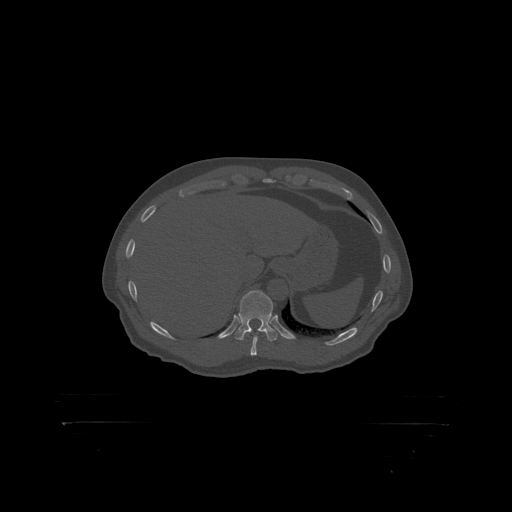
CT including the spine, one axial slice. Position 386 of 399 along the scan axis. 120 kVp. Bone window (W 1800 / L 400 HU). 1.25 mm slice thickness. 512 × 512 image matrix, field of view 650 × 650 mm. Patient: male, 46 years. Case-level facts recorded for this patient, not image findings: primary cancer: skin.
Outlined on this slice (semi-automatic segmentation, software-assisted and operator-edited):
- T11 vertebra: box from (x=239, y=290) to (x=274, y=319) px